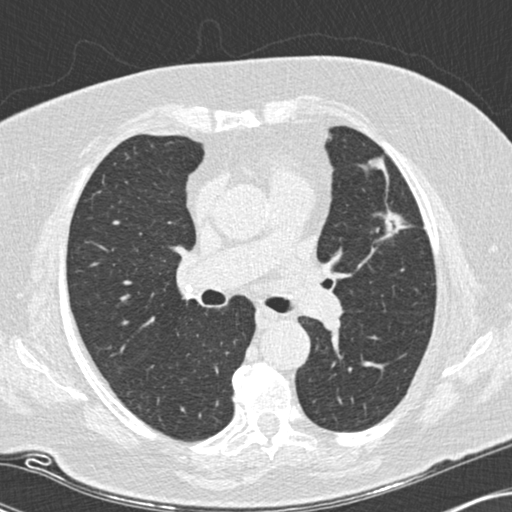
Low-dose screening chest CT, one axial slice. Slice 96 of 151 in the series (ordered by position). Reconstruction kernel B30f. 120 kVp. Lung window (W 1500 / L -600 HU). 2 mm slice thickness. 512 × 512 image matrix, field of view 330 × 330 mm.
Structures marked on this image (outlined manually by an expert reader):
- lesion 1 (tumor, upper lobe of left lung): box from (x=379, y=210) to (x=409, y=240) px